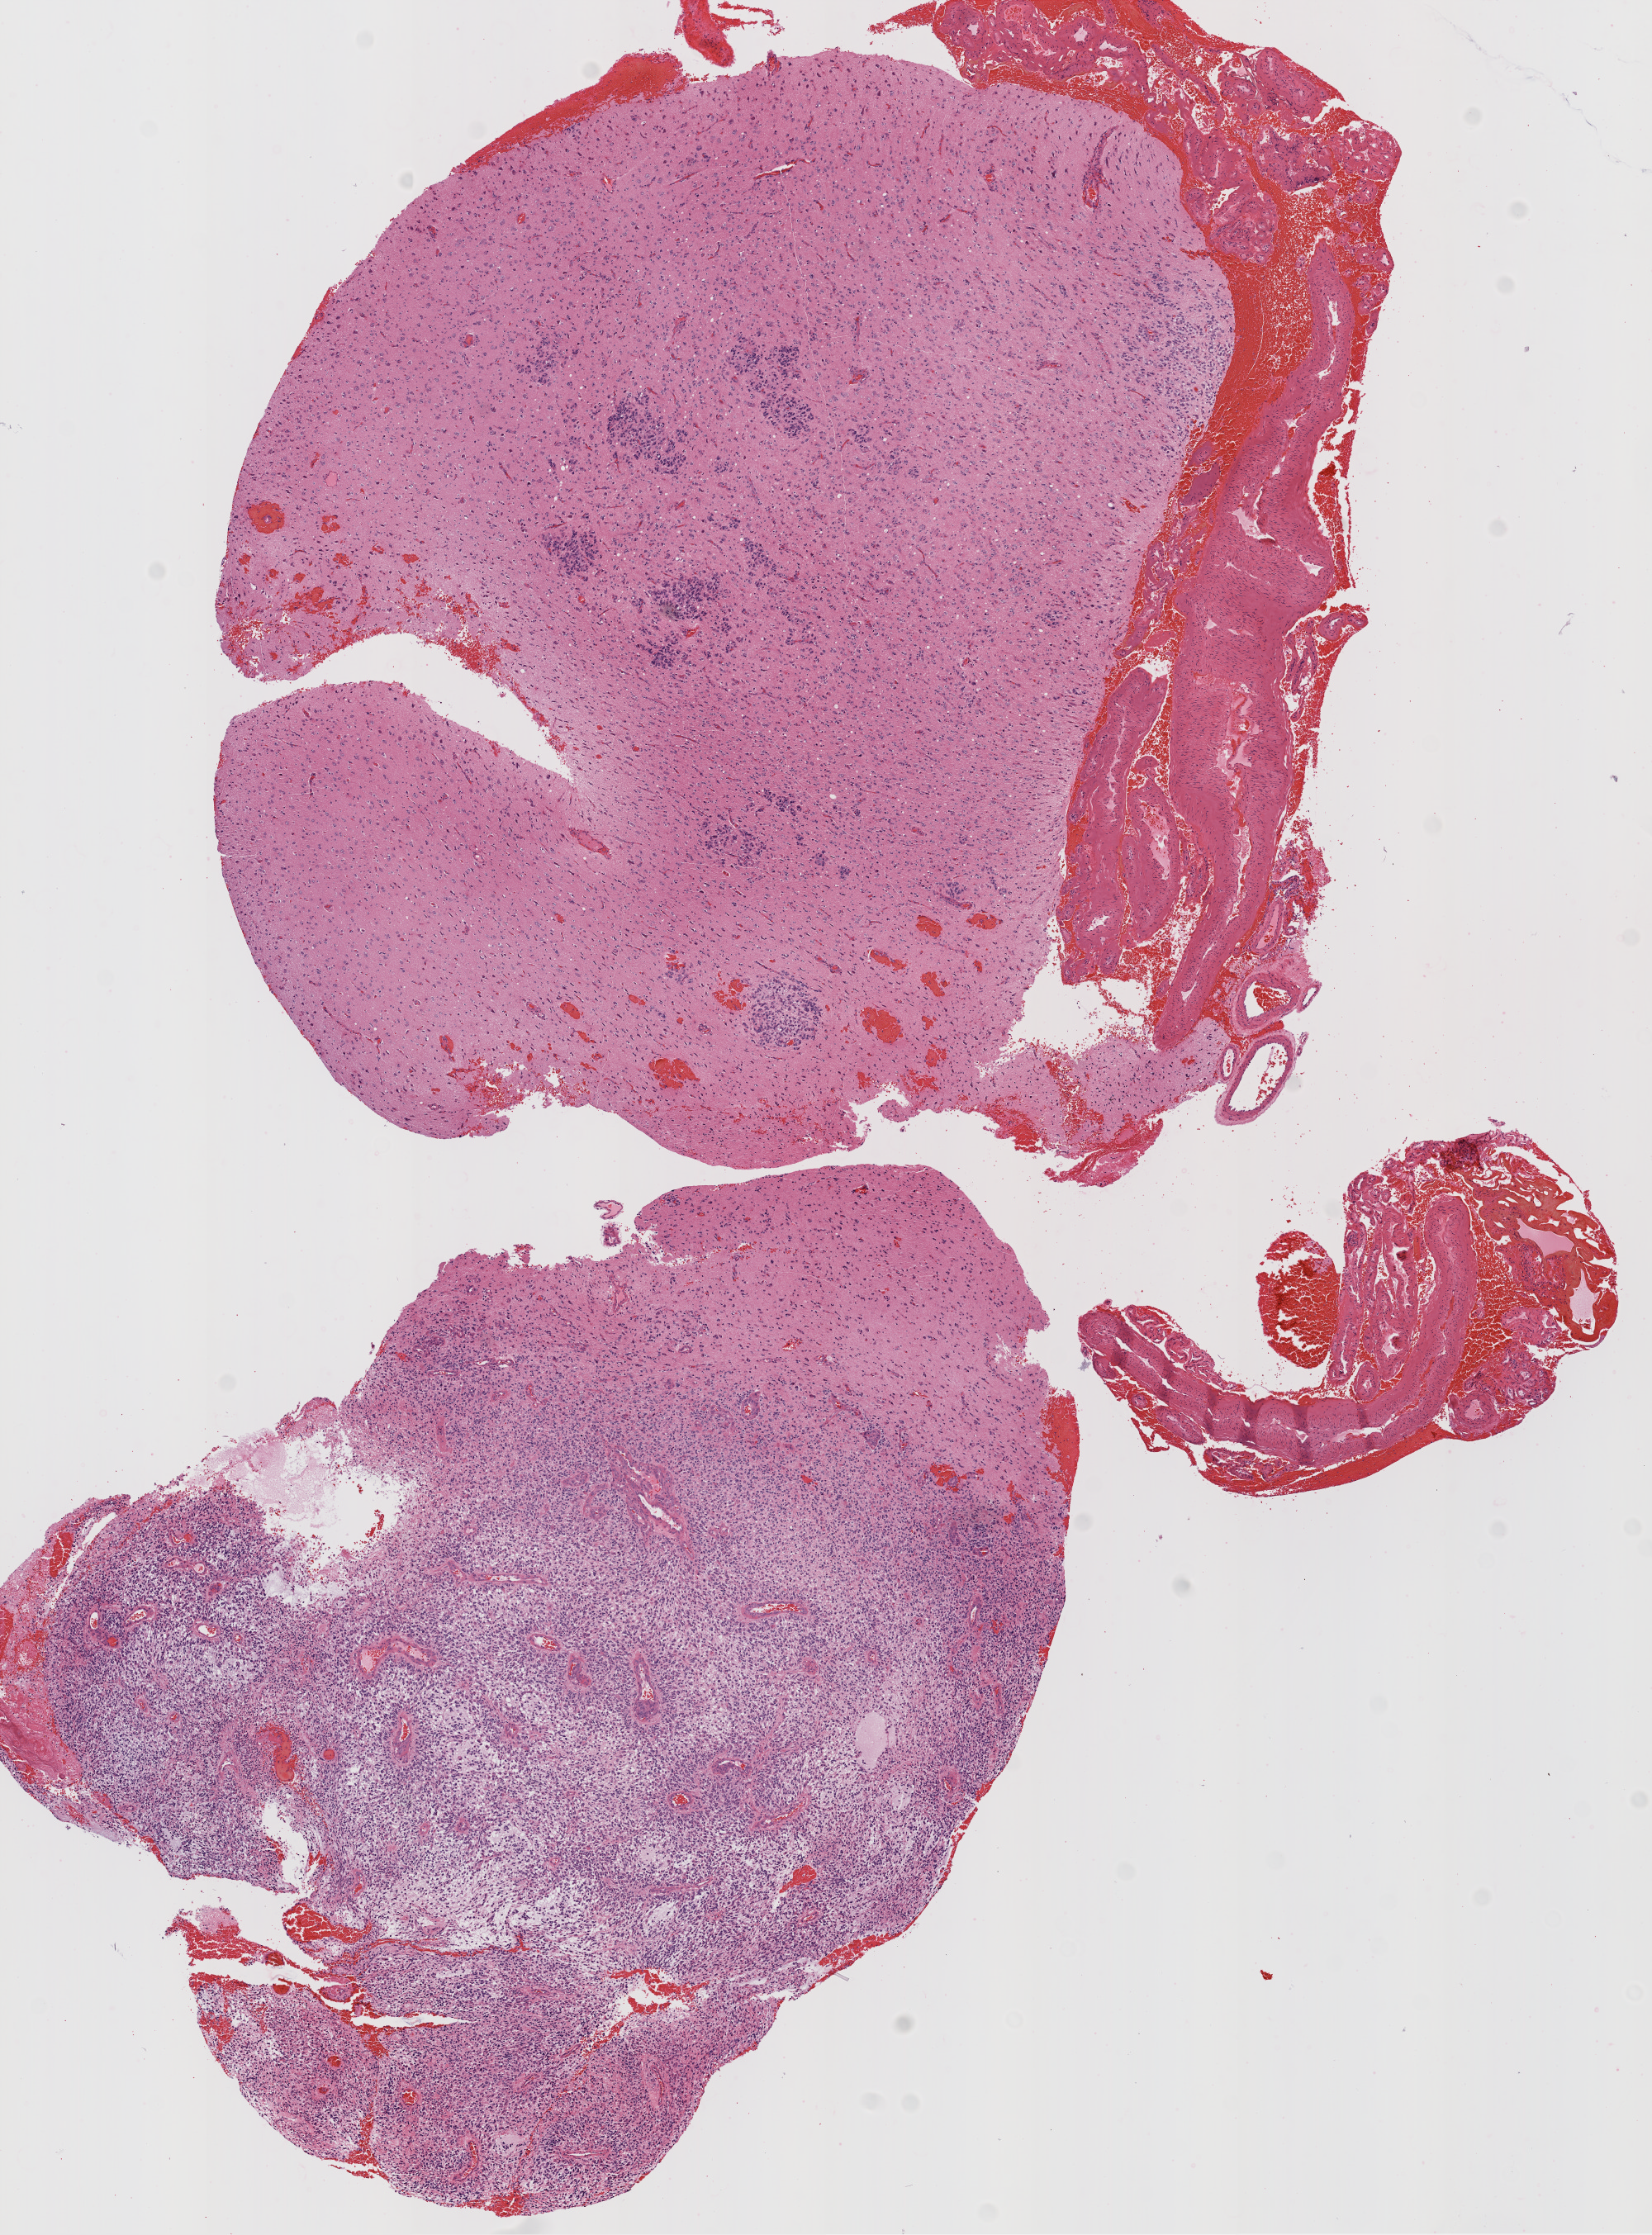
H&E-stained whole-slide image, shown as a low-resolution overview of the whole scanned area (about 8.0 x 10.9 mm, slide scanned at 20x); FFPE section; primary tumour sample from the brain. Male, age 54 years at initial diagnosis.
* diagnosis: Glioblastoma